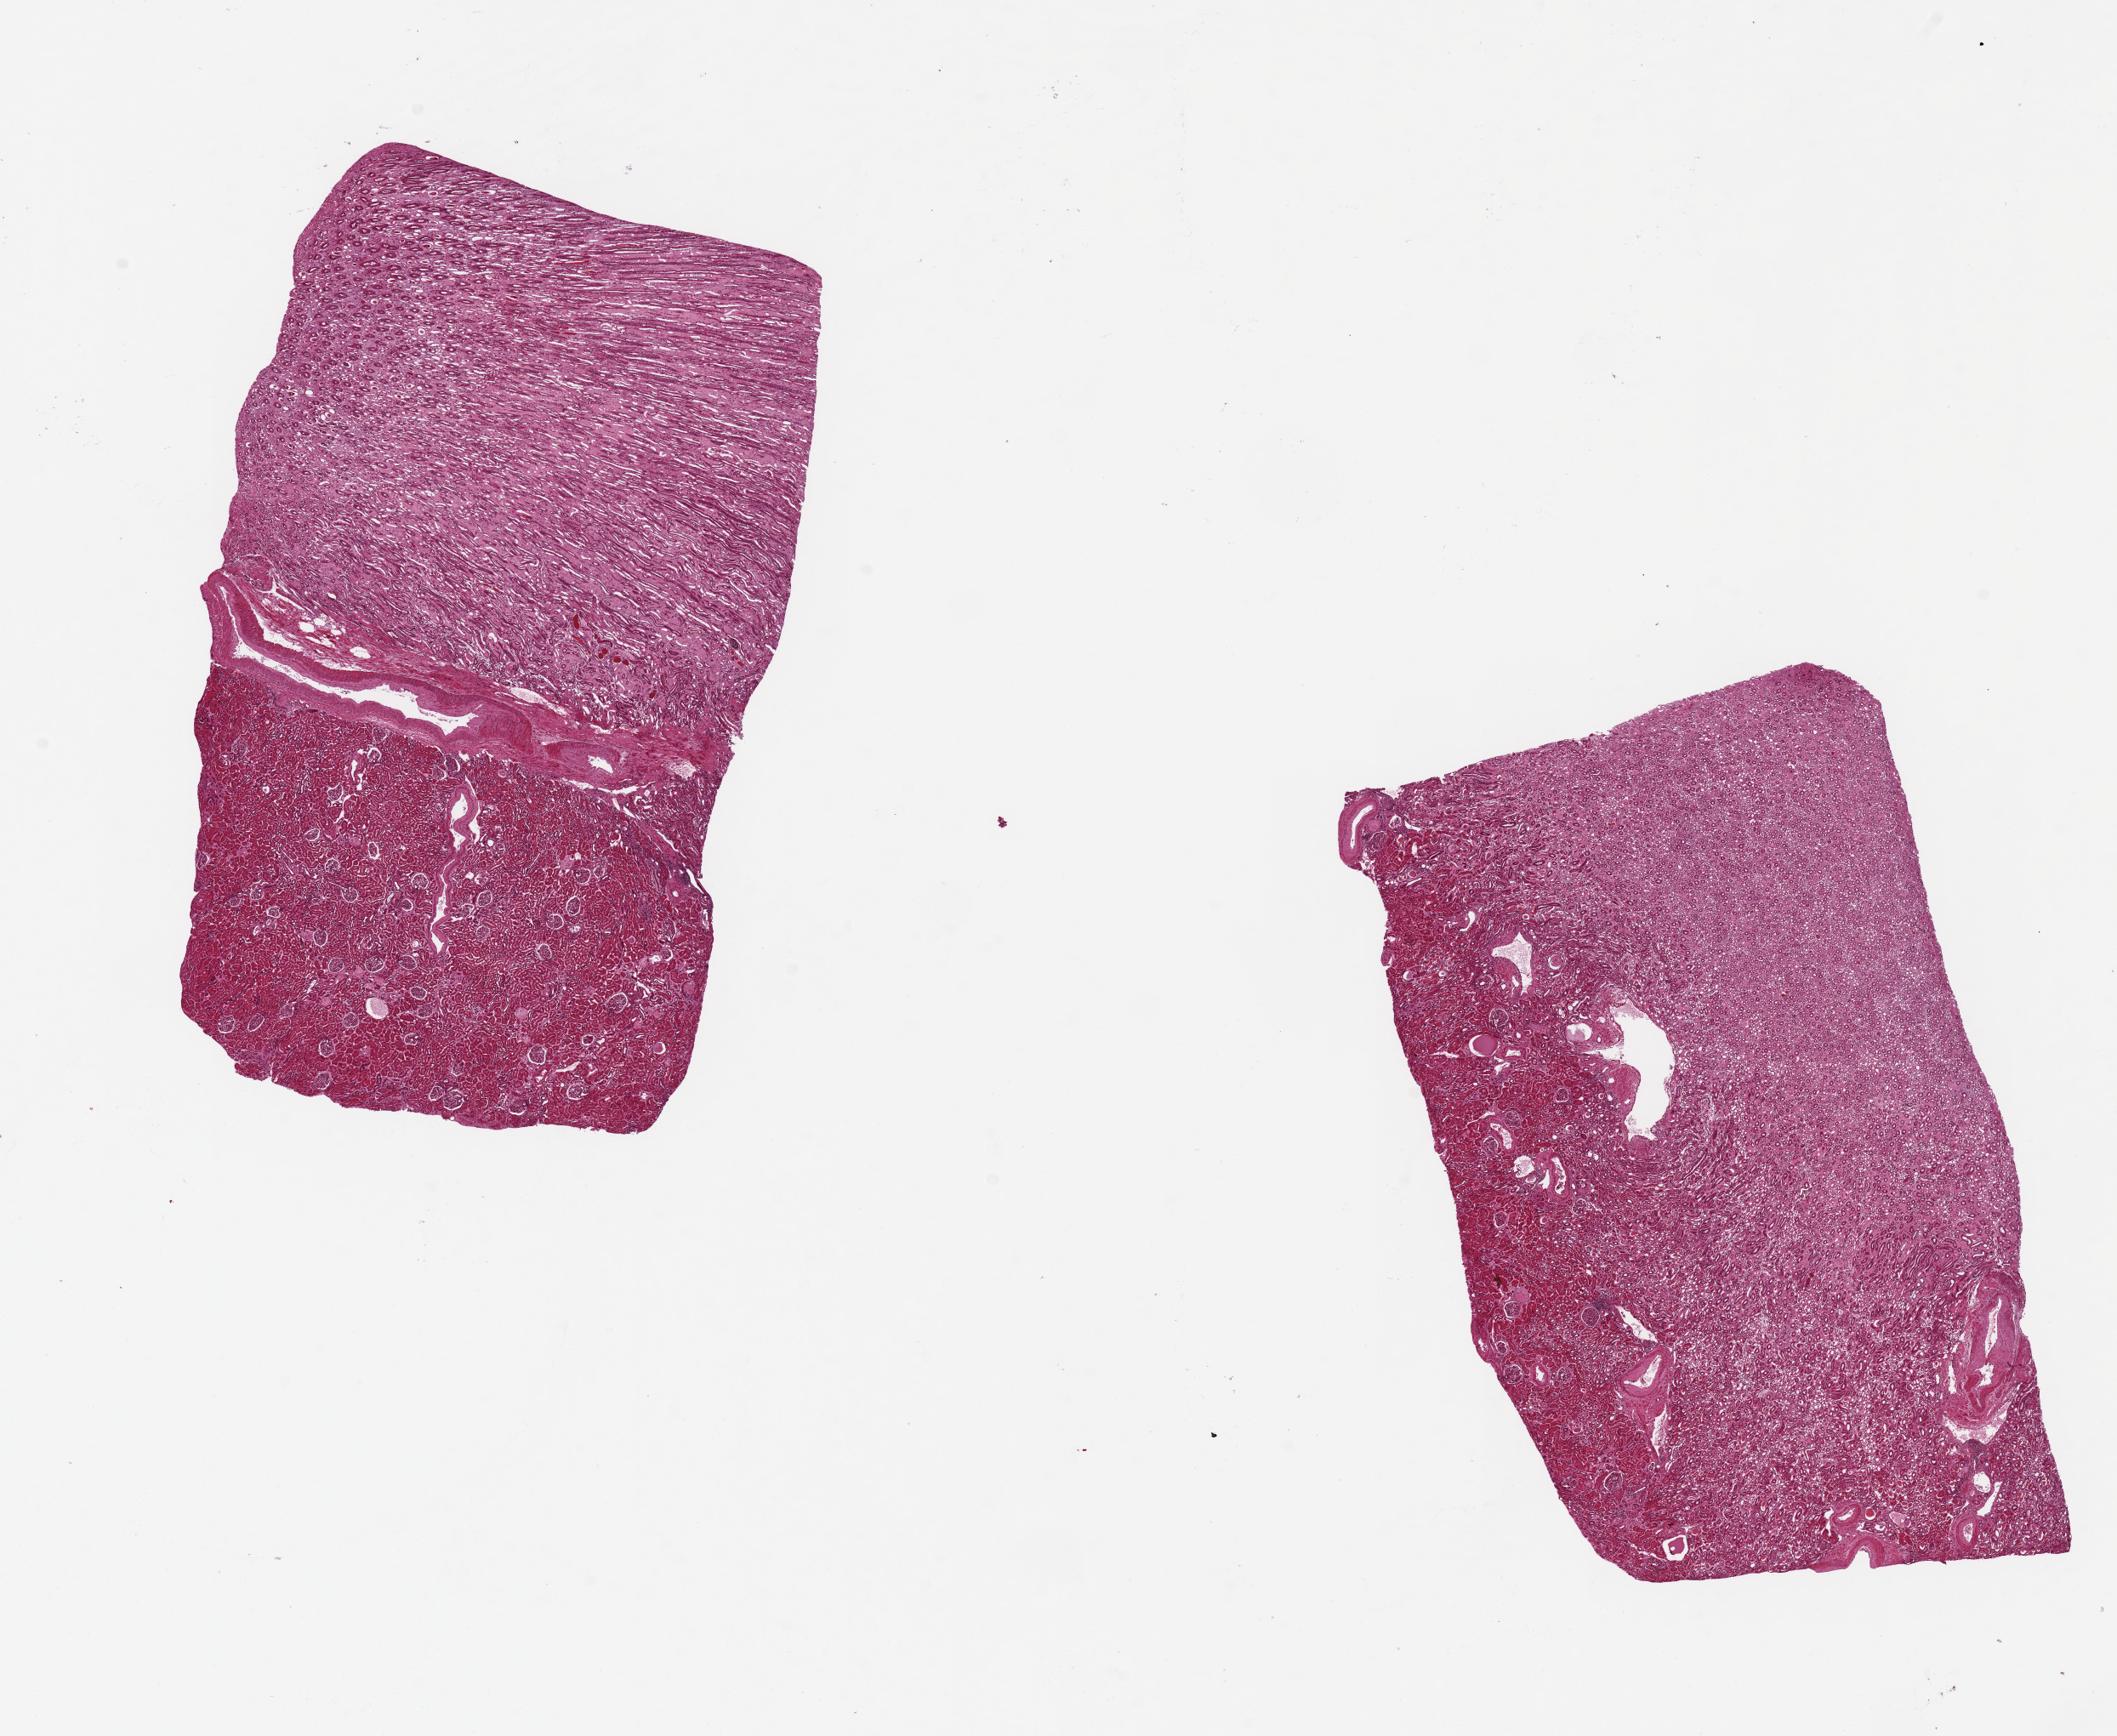
Haematoxylin and eosin whole-slide image, brightfield — shown as a low-resolution overview of the whole scanned area (about 19.7 x 16.1 mm); PAXgene-fixed paraffin-embedded (PFPE) section; sampled site (target tissue): renal medulla; donor tissue sample. Male donor.
* pathologist's review note for this sample: 2 pieces, ~8x5mm. NOTE: Each aliquot is ~40% cortex